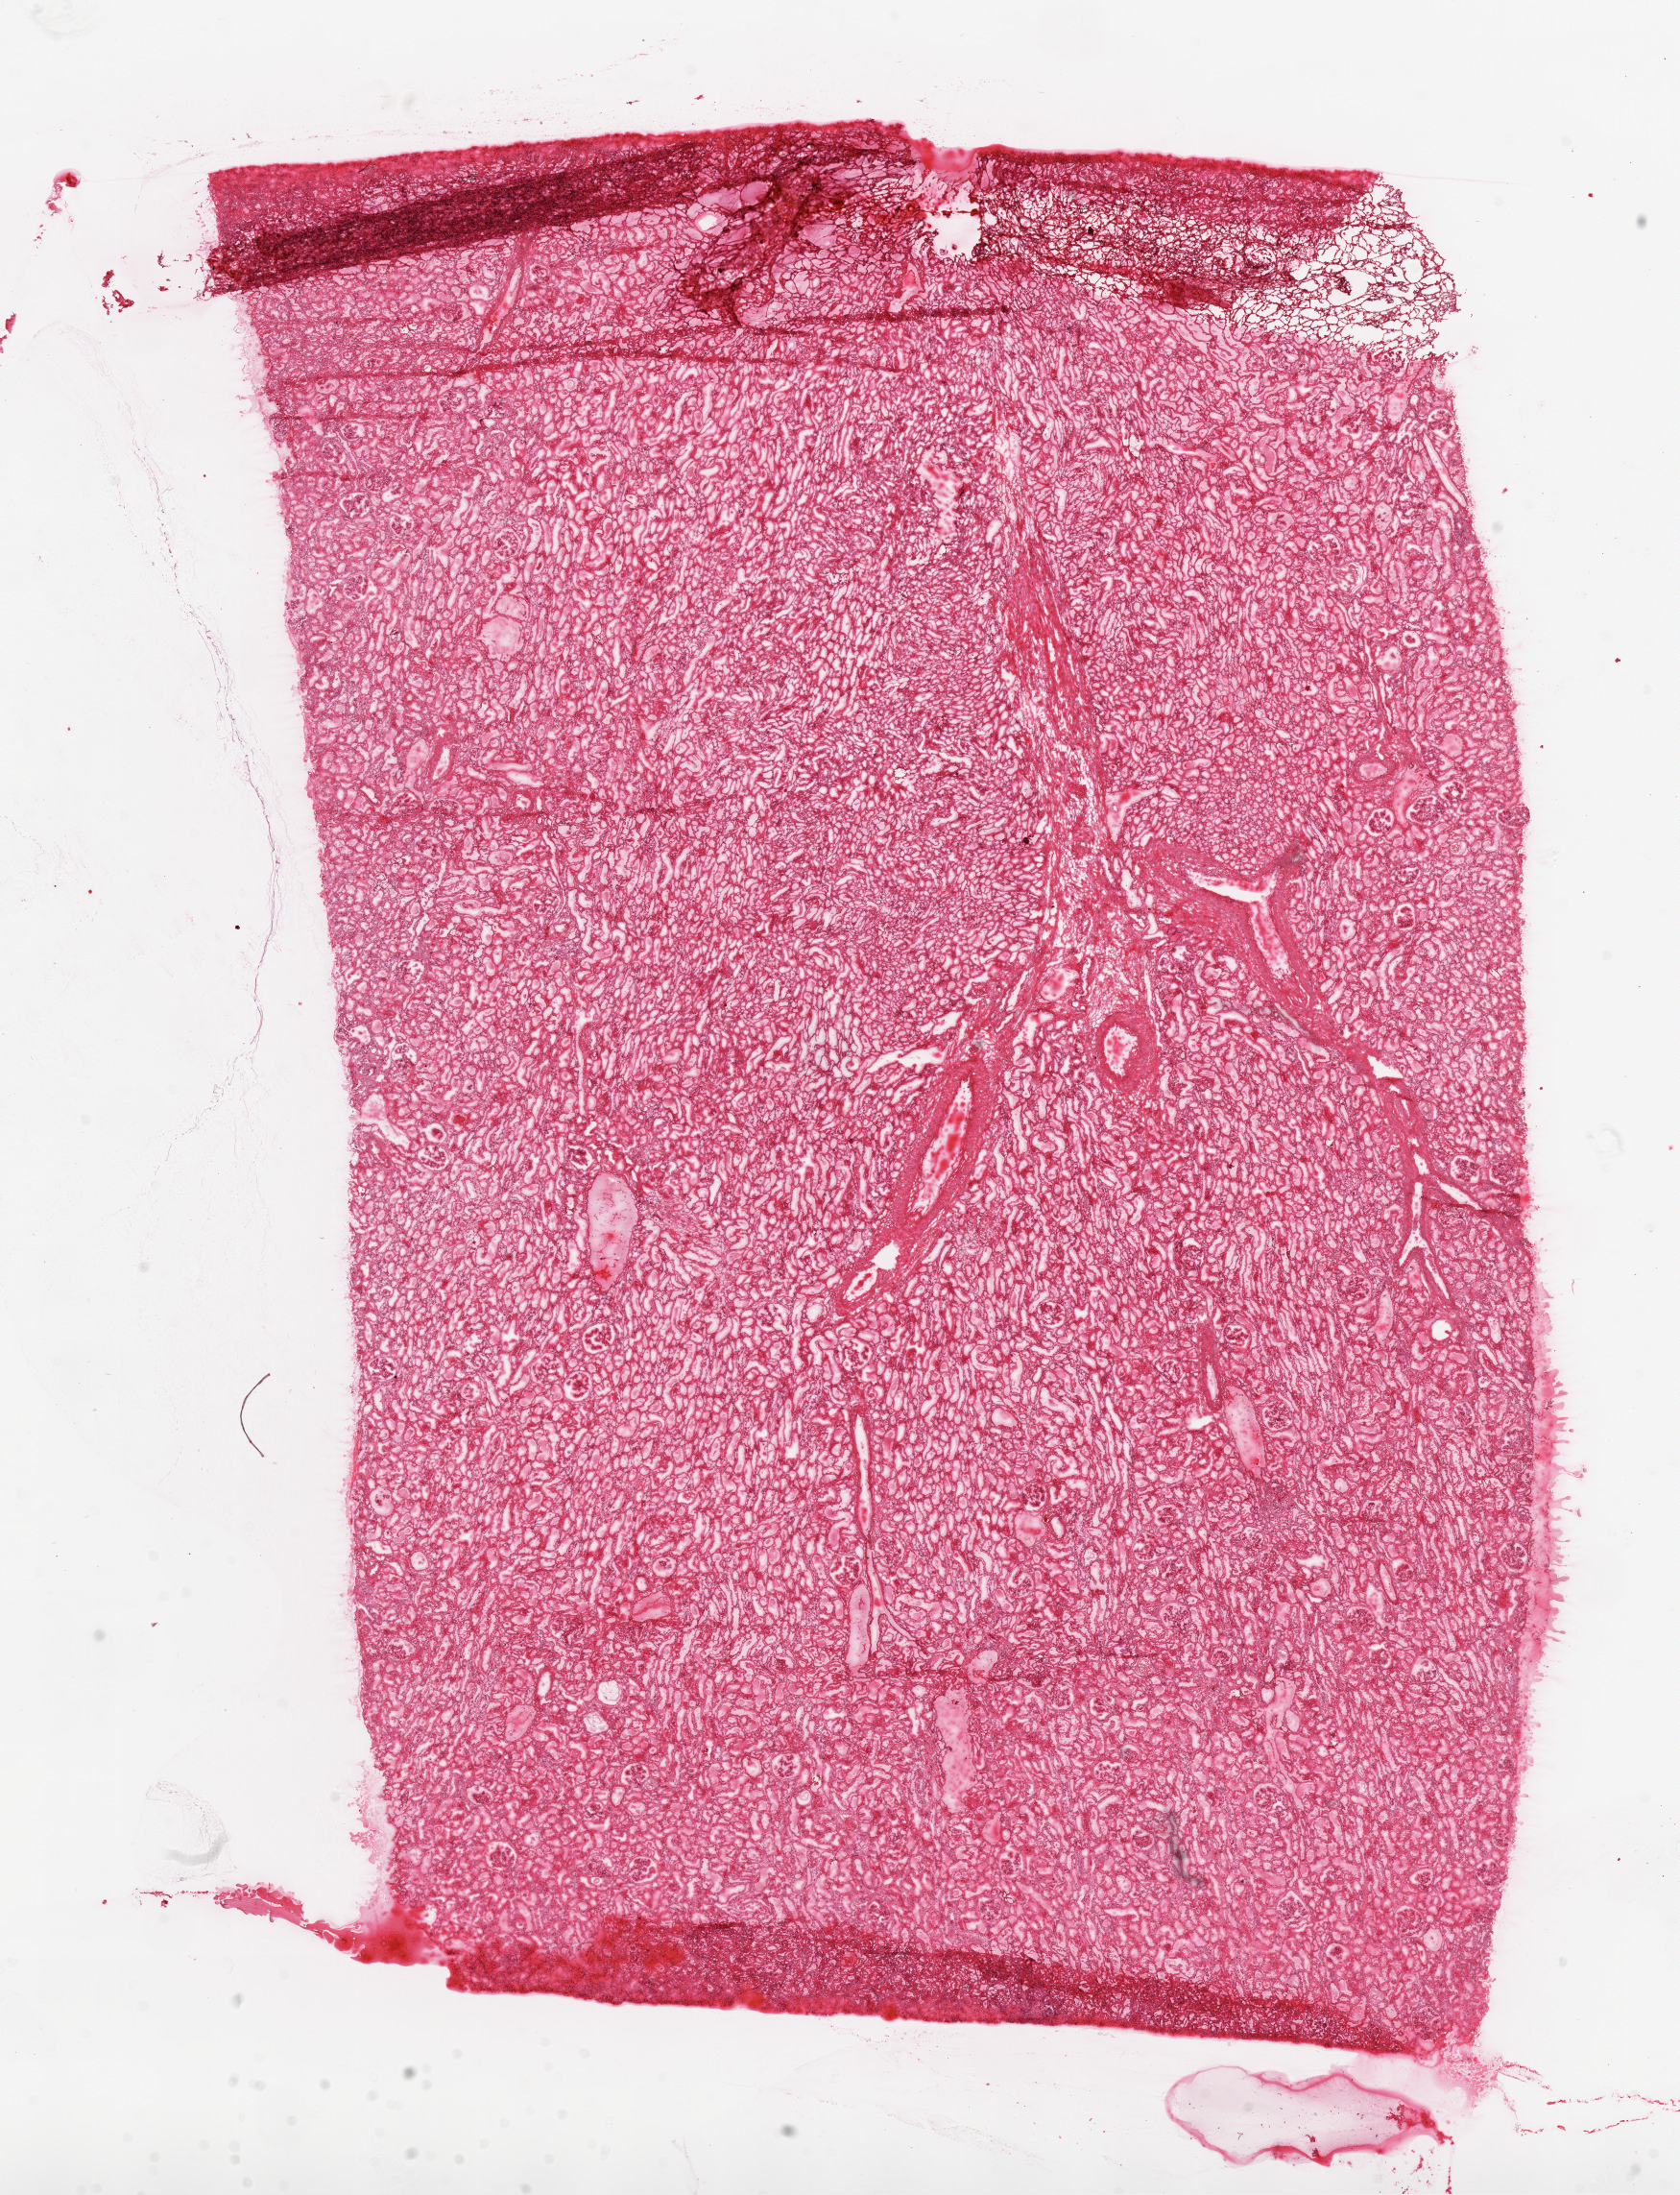
H&E whole-slide image, whole scanned area (about 14.0 x 18.3 mm, from a 20x scan) shown as a low-resolution overview; frozen section; sample: solid tissue normal (non-tumour tissue), kidney. Female, age 51 years at initial diagnosis.
- this section: solid tissue normal sample (biorepository sample class)
- patient diagnosis: Clear cell adenocarcinoma, NOS